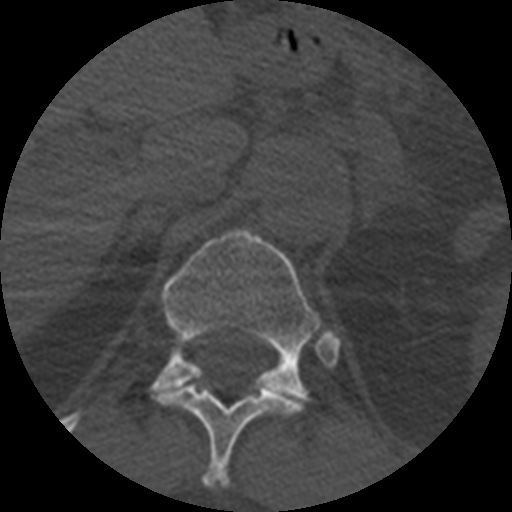
CT including the spine, one axial slice. Position 397 of 399 along the scan axis. Reconstruction kernel STANDARD. Bone window (W 1800 / L 400 HU). 512 × 512 image matrix. Patient age 71 years. From the clinical record (not read from this slice): primary cancer: prostate.
Annotated regions visible in this slice (semi-automatic segmentation, software-assisted and operator-edited):
- T11 vertebra: bounding box (x1, y1, x2, y2) in pixels: (154, 386, 302, 488)
- T12 vertebra: (151, 228, 339, 406)